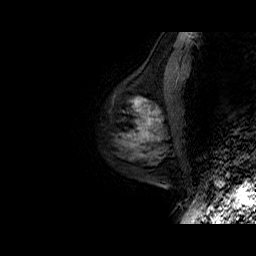
Breast MRI (dynamic contrast-enhanced), one sagittal slice; position 16 of 50 along the scan axis; dynamic contrast-enhanced series, time point 2 of 6 at this slice position (early post-contrast); 1.5 T; TE 6.5 ms, TR 32.9 ms; 4 mm slice thickness; 256 × 256 image matrix, field of view 200 × 200 mm. Female patient. Case-level facts recorded for this patient, not image findings: setting: breast cancer imaged before/during neoadjuvant chemotherapy; receptor status: HR-positive, HER2-negative.
Outlined on this slice (semi-automatically segmented with operator editing):
- analysis volume of interest (the breast-tissue region the enhancement analysis was run in; not a lesion): box from (x=115, y=75) to (x=177, y=149) px
- tumour enhancement mask (voxels above the 100 % enhancement threshold inside the analysis volume of interest): (x=134, y=99)–(x=160, y=141)